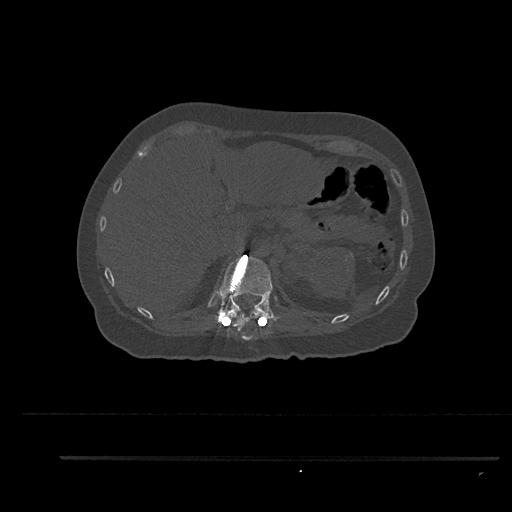
CT including the spine, one axial slice. Position 282 of 797 along the scan axis. Reconstruction kernel Br40s/3. 120 kVp. Bone window (W 1800 / L 400 HU). 0.5 mm slice thickness. 512 × 512 image matrix, field of view 408 × 408 mm. Patient: female, 44 years. From the clinical record (not read from this slice): primary cancer: renal.
Structures marked on this image (semi-automatically segmented with operator editing):
- T11 vertebra: bounding box [x1, y1, x2, y2] px = [232, 310, 255, 340]
- T12 vertebra: [219, 246, 282, 326]